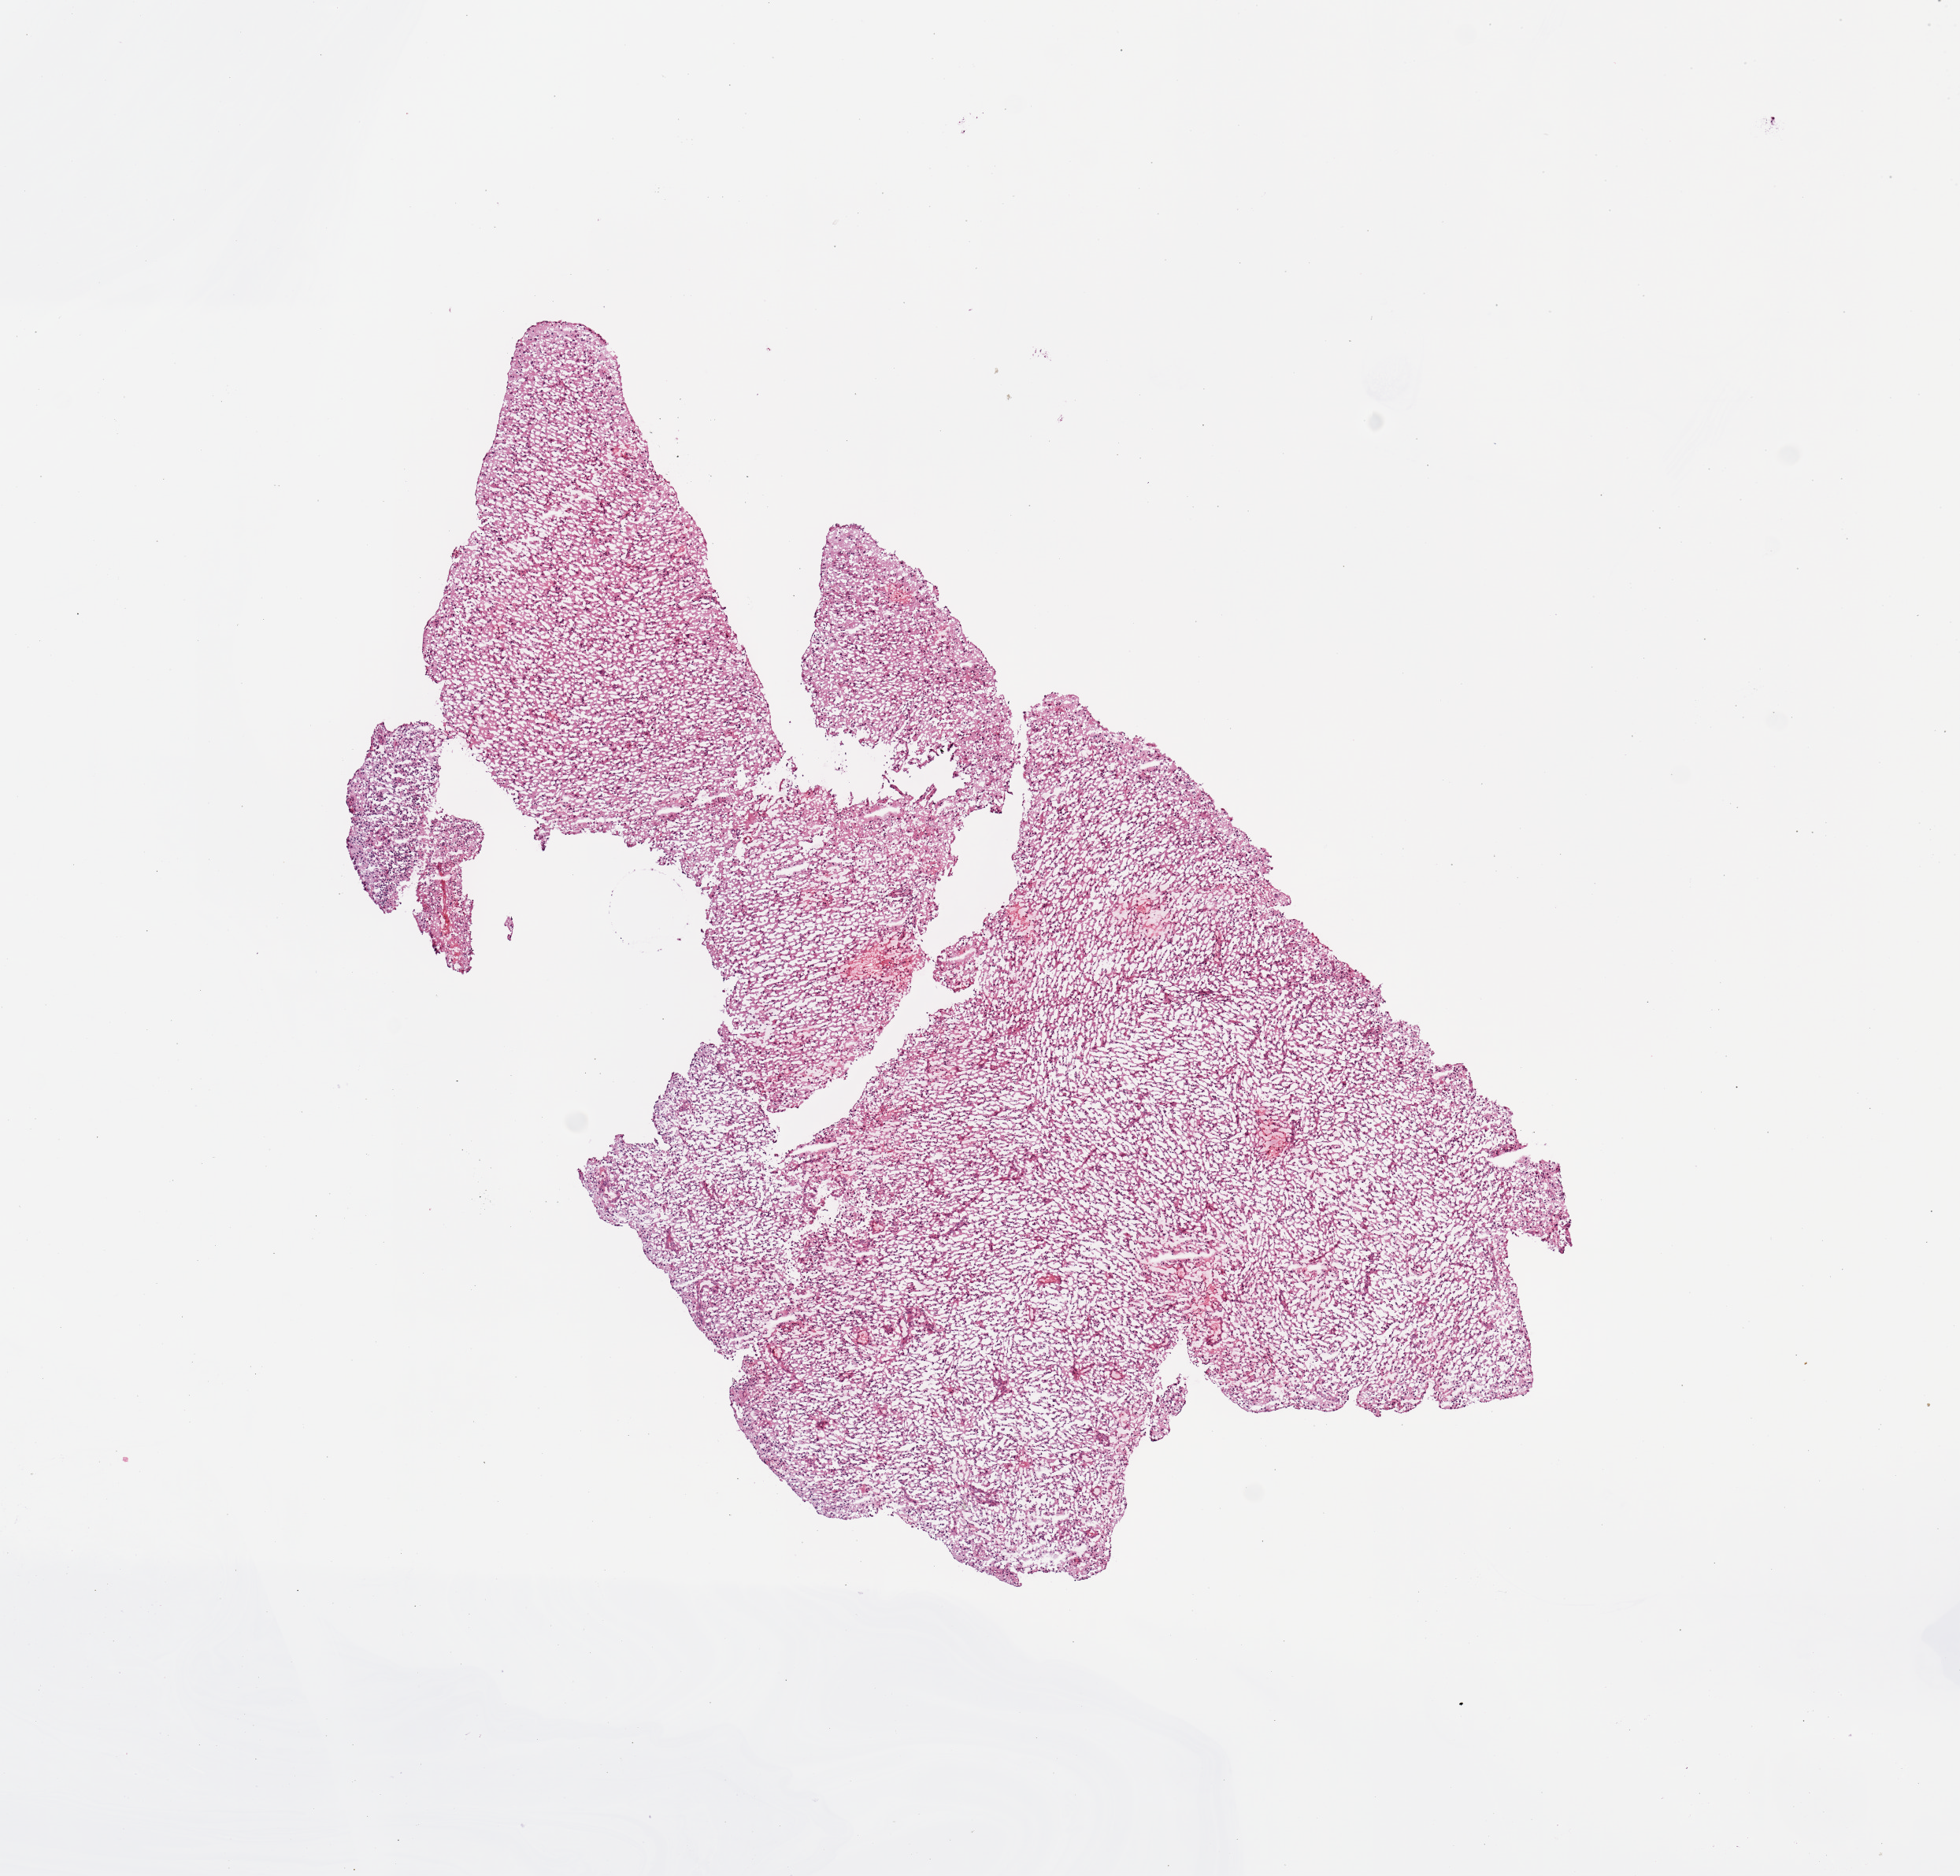
H&E whole-slide image — a low-resolution overview of the entire scanned area, about 9.8 x 9.4 mm; brain, tumour tissue. Male, 65 y/o.
Patient diagnosis (cohort enrolment): glioblastoma multiforme (brain).